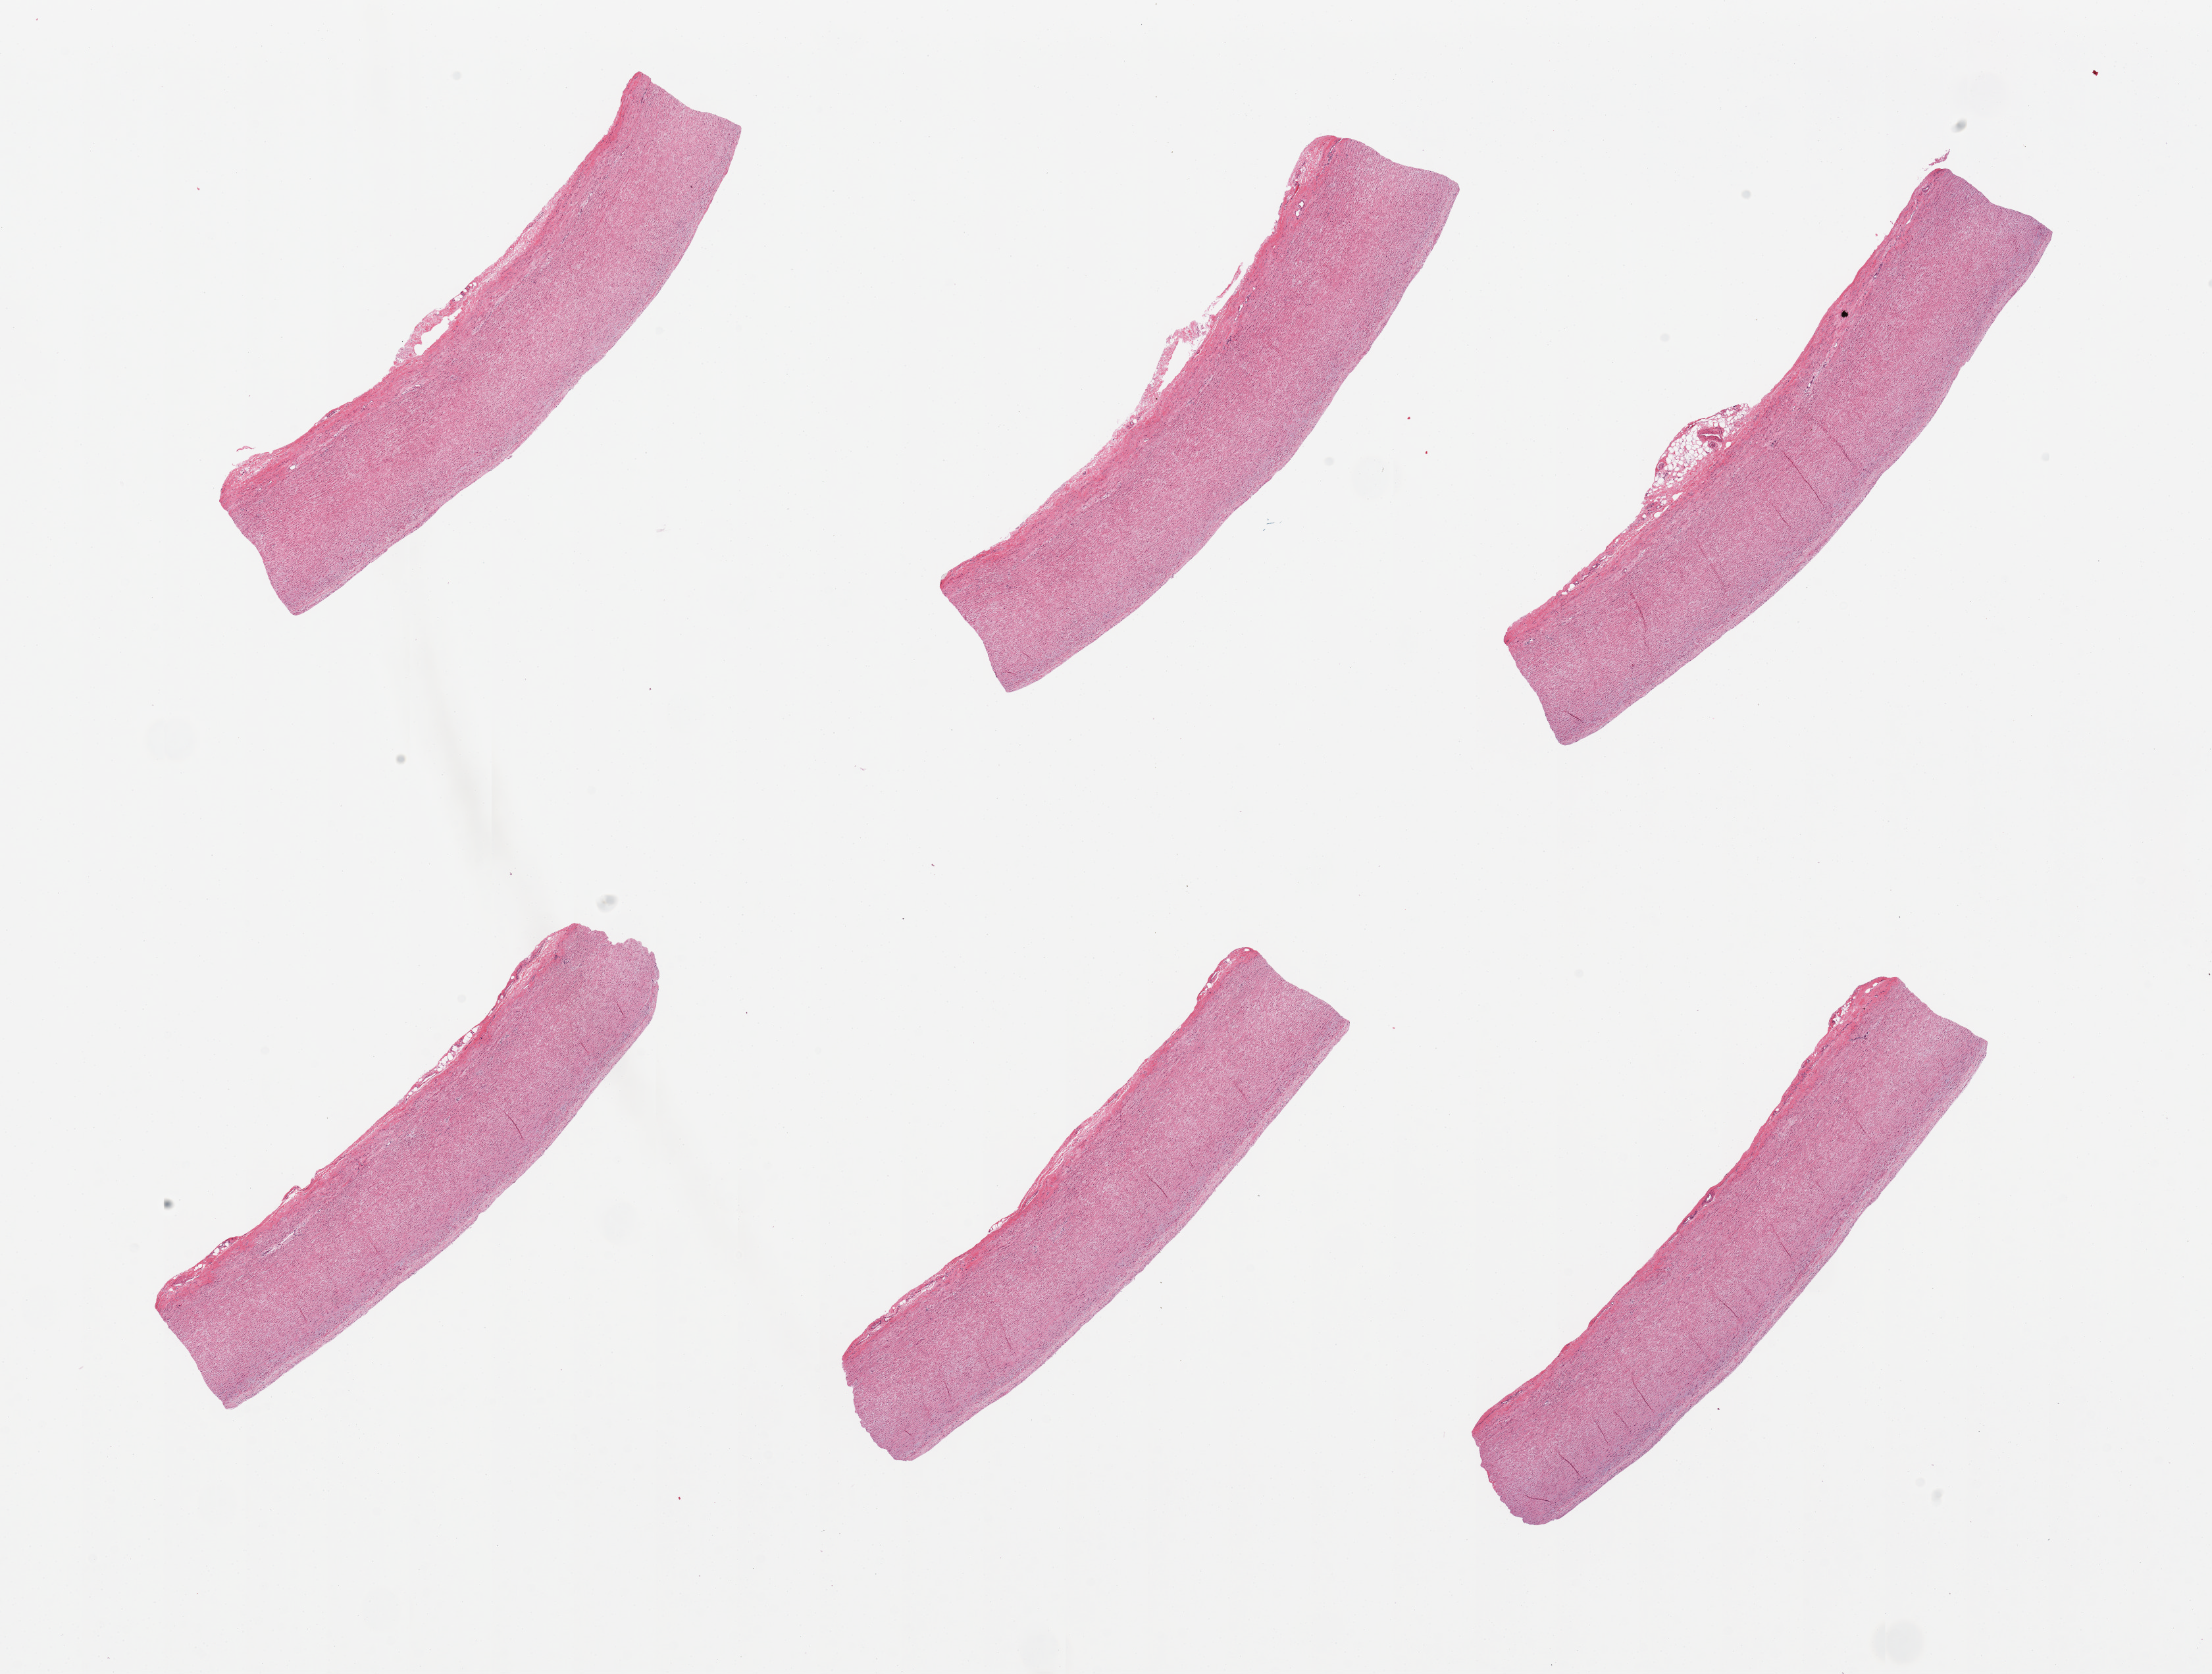
Whole-slide image, haematoxylin and eosin stain — low-resolution overview of the scanned area, about 26.6 x 20.1 mm (from a 20x scan), PAXgene-fixed paraffin-embedded (PFPE) section, sampled site (target tissue): aorta, donor tissue sample. Donor: female.
Review note (as recorded): 6 pieces, minimal atherosis.